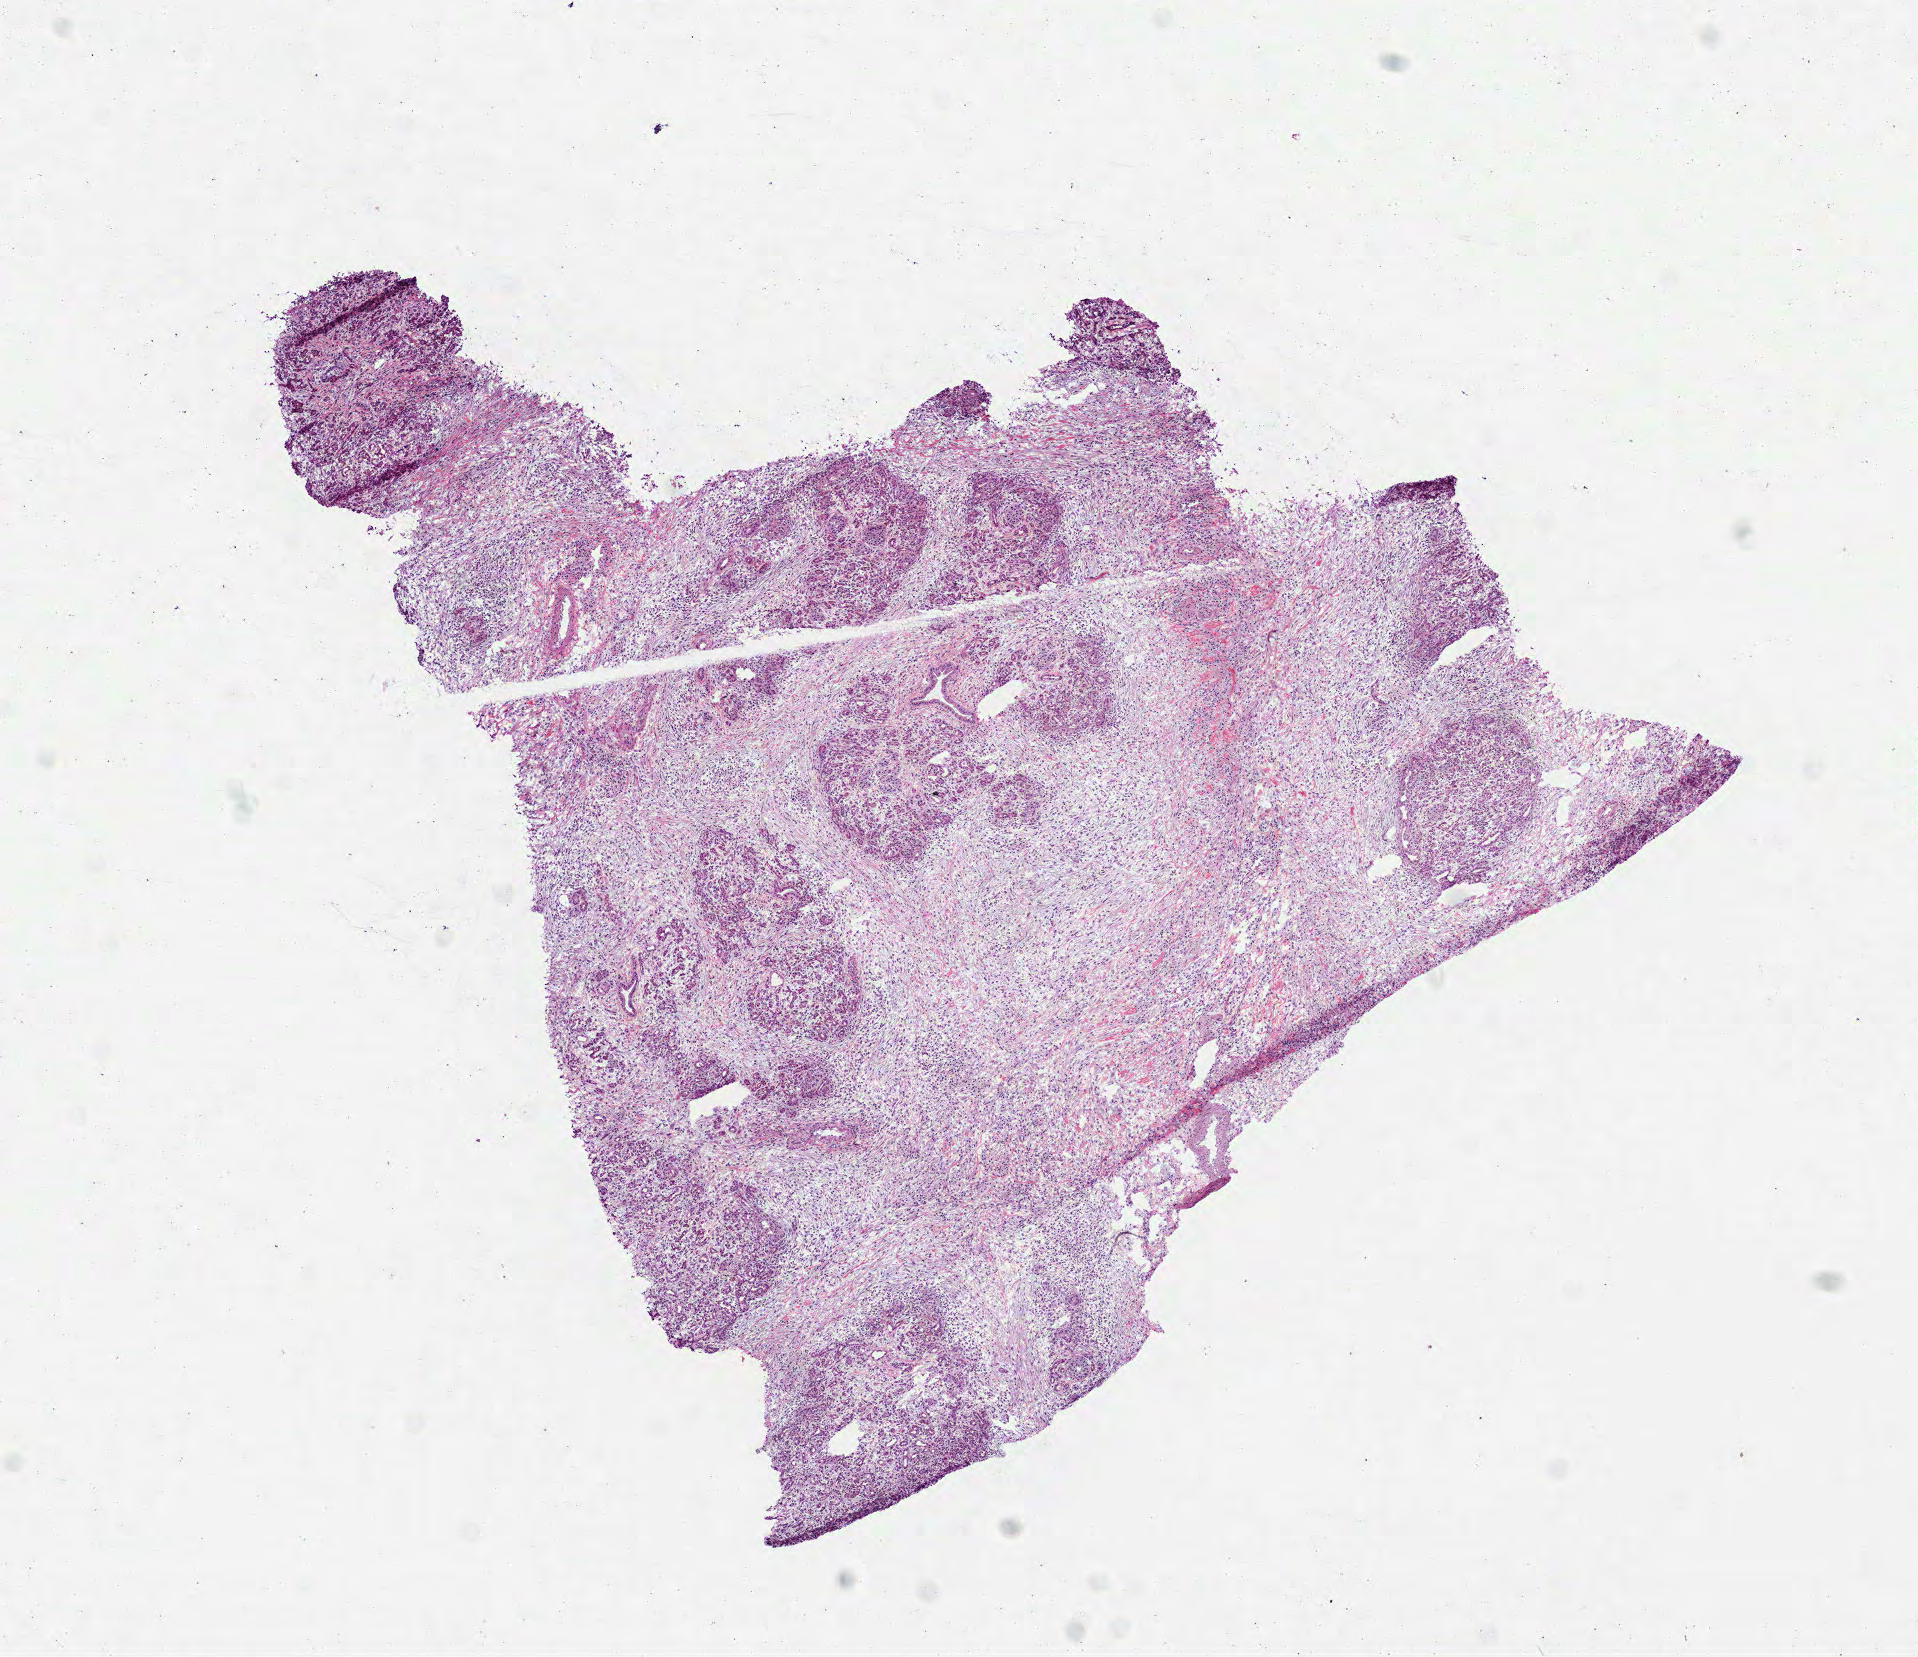
H&E-stained whole-slide image — whole scanned area (about 7.7 x 6.7 mm, from a 40x scan) shown as a low-resolution overview; frozen section; sample: solid tissue normal (non-tumour tissue), pancreas. Female patient; age at initial diagnosis 56 years. Inflammatory infiltration, as recorded: lymphocyte infiltration 10%, monocyte infiltration 0%, neutrophil infiltration 0%.
• this section: solid tissue normal sample (biorepository sample class)
• patient diagnosis: Adenocarcinoma, NOS (head of pancreas)